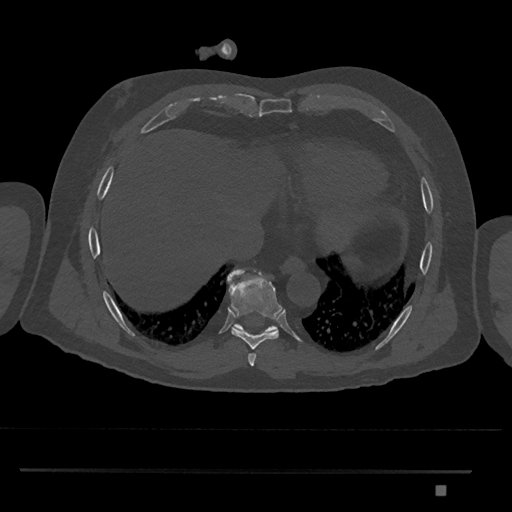
CT including the spine, one axial slice; position 1096 of 1134 along the scan axis; reconstruction kernel Br40s/3; 120 kVp; bone window (W 1800 / L 400 HU); 0.5 mm slice thickness; 512 × 512 image matrix, field of view 429 × 429 mm. Male patient, age 65 years. Case-level facts recorded for this patient, not image findings: primary cancer: prostate.
Structures marked on this image (semi-automatically segmented with operator editing):
- T8 vertebra: bounding box <228,269,284,349> (left, top, right, bottom; pixels)
- T9 vertebra: <227,271,278,333>